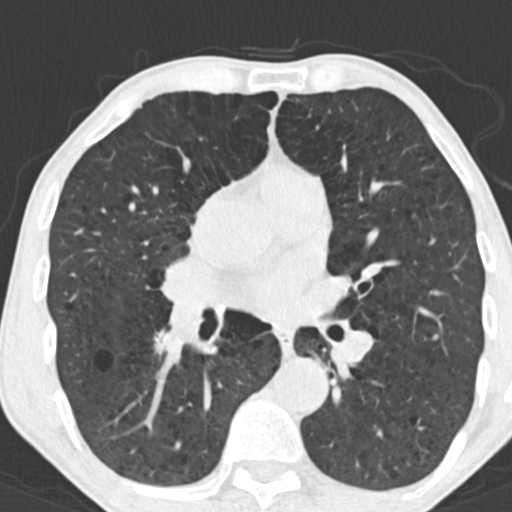
Low-dose screening chest CT, axial slice; baseline annual screen; lung window (W 1500 / L -600 HU); slice 93 of 180 in the series; 512 × 512 image matrix, field of view 286 × 286 mm. Male, age 64 years at enrolment. Current smoker at enrolment.
Lesion marked by an expert reader, bounding box [x1, y1, x2, y2] px = [134, 315, 190, 363]. Screening reader's record for this exam: no non-calcified nodule ≥4 mm recorded. Later outcome: lung cancer diagnosed 386 days after this screen — adenocarcinoma, NOS, right lower lobe, stage IV (AJCC 6th edition), 60 mm at pathology.